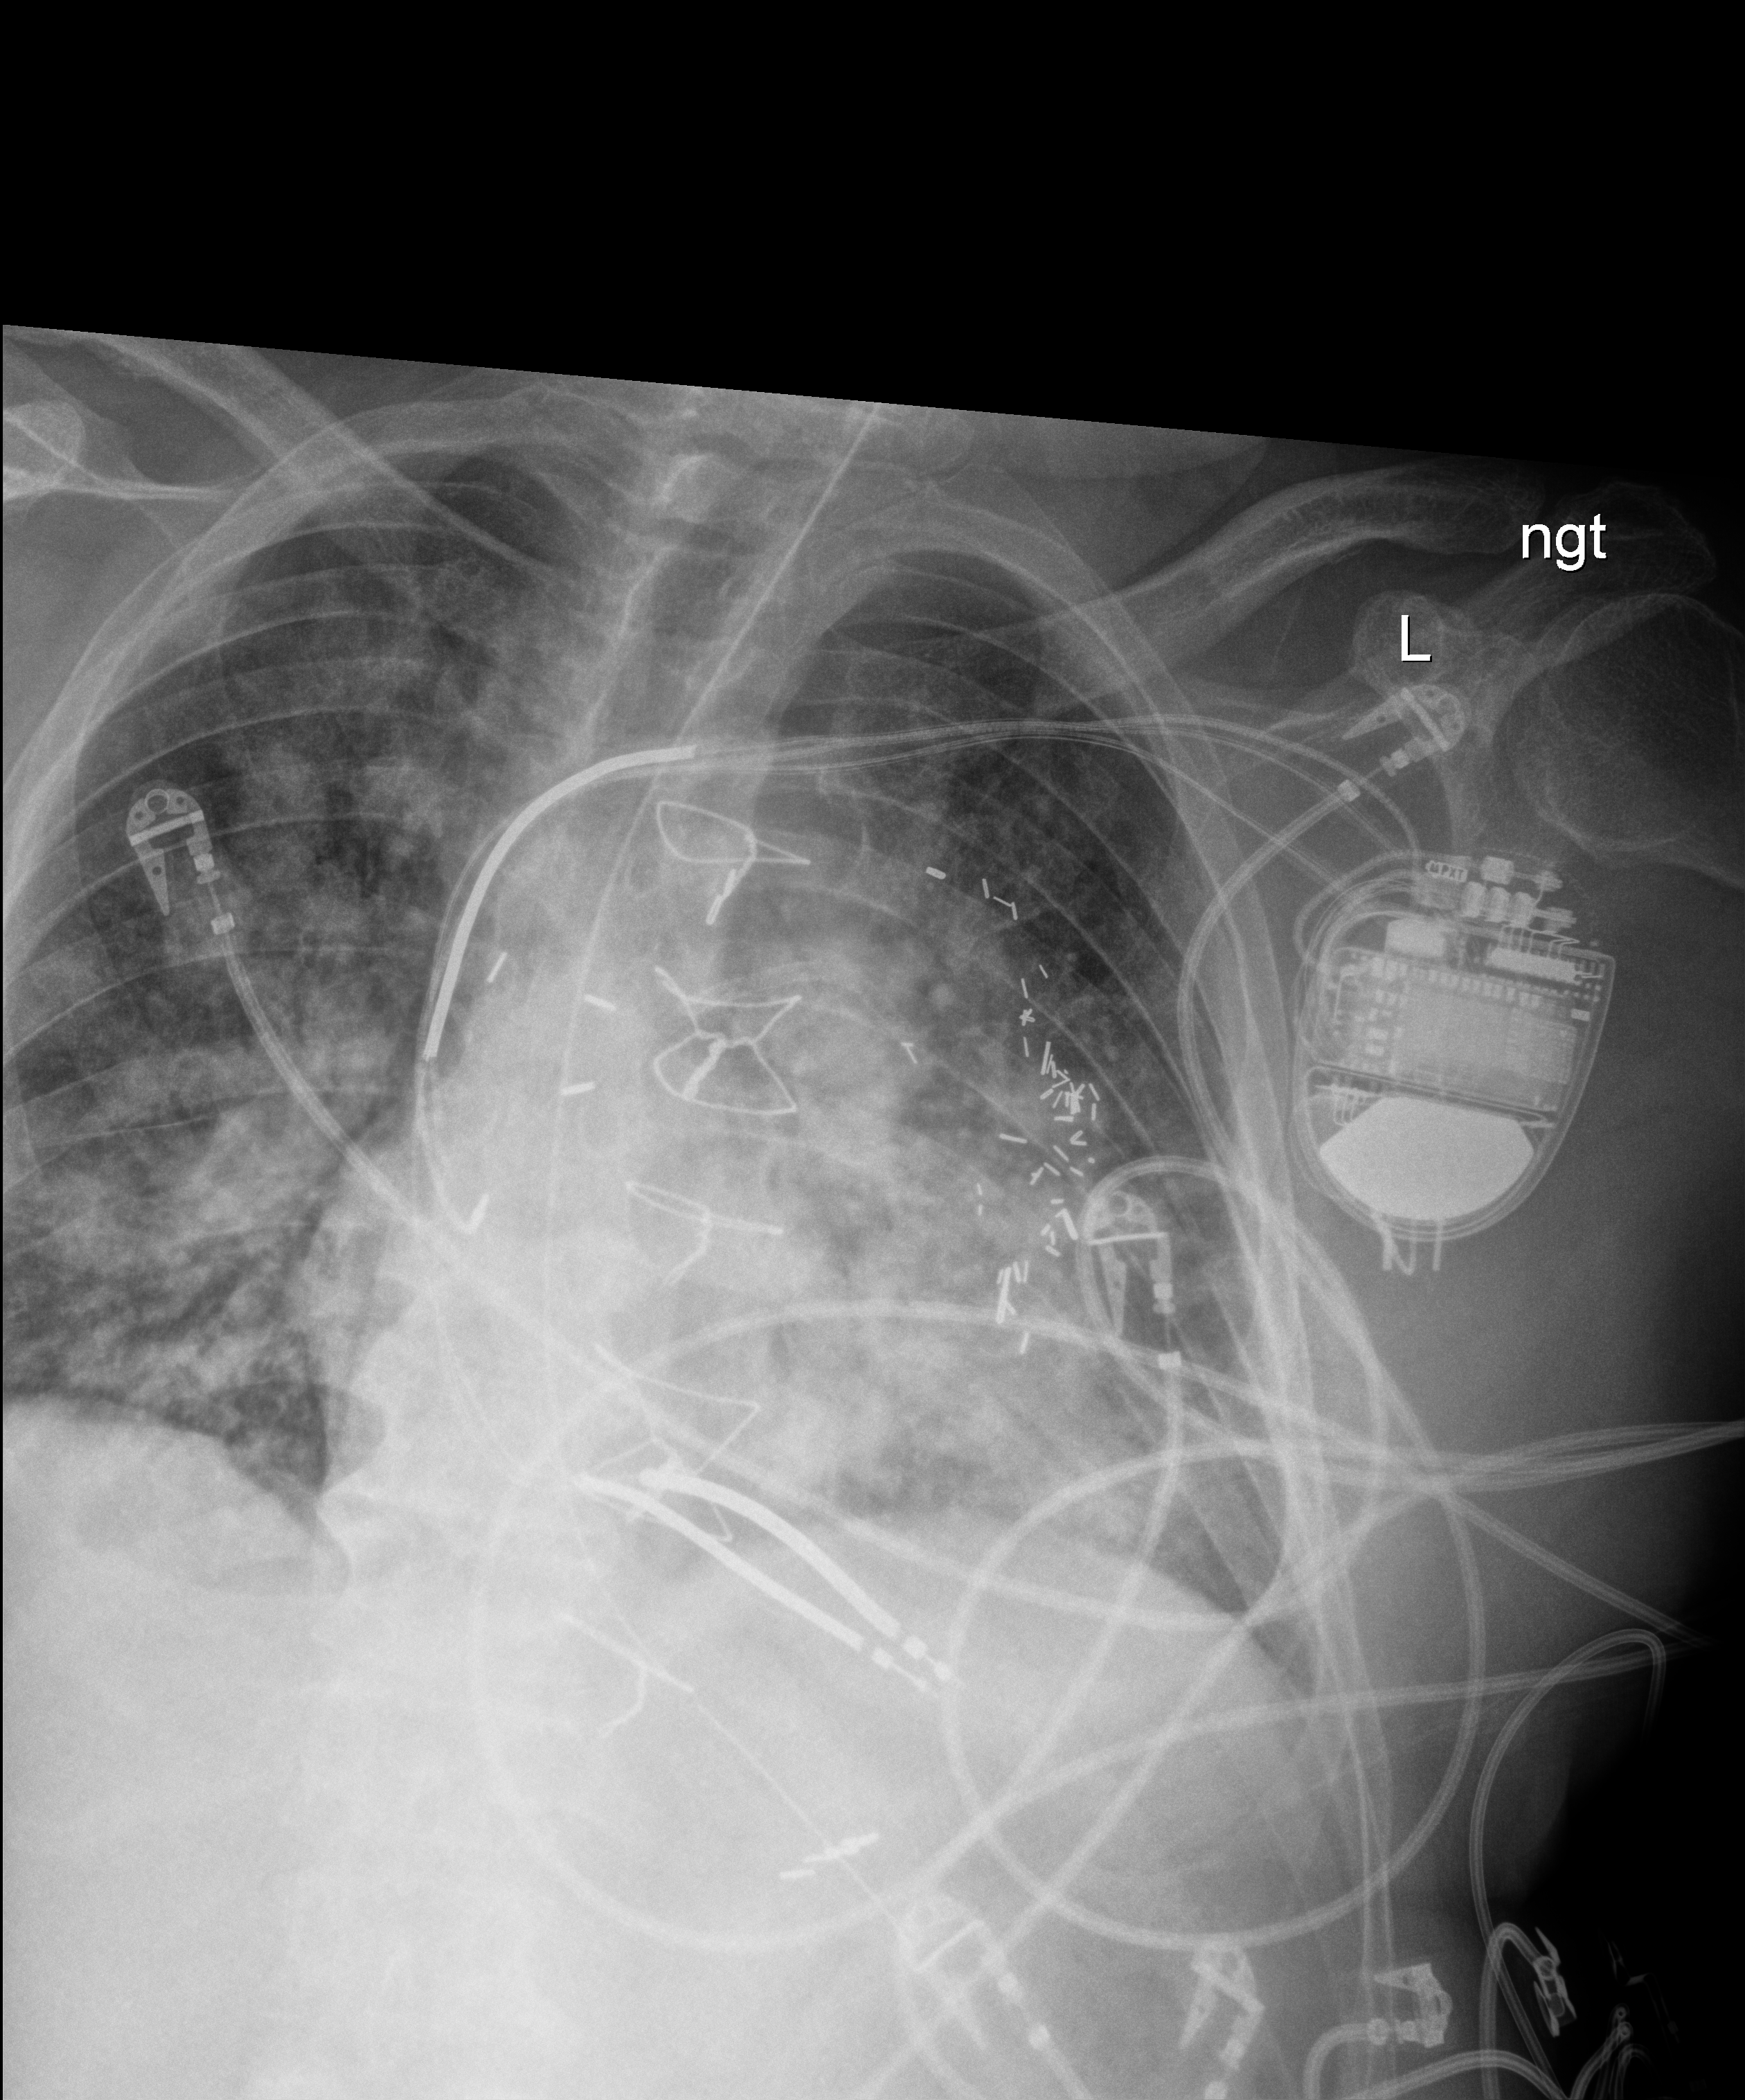
Chest X-ray (portable); anteroposterior (AP) projection. Male patient hospitalised with COVID-19, age 60–74 years.
Hospital-stay facts (about this admission, not read from this image; timing relative to this image not recorded): hypertension (admission record): yes; COPD (admission record): no.